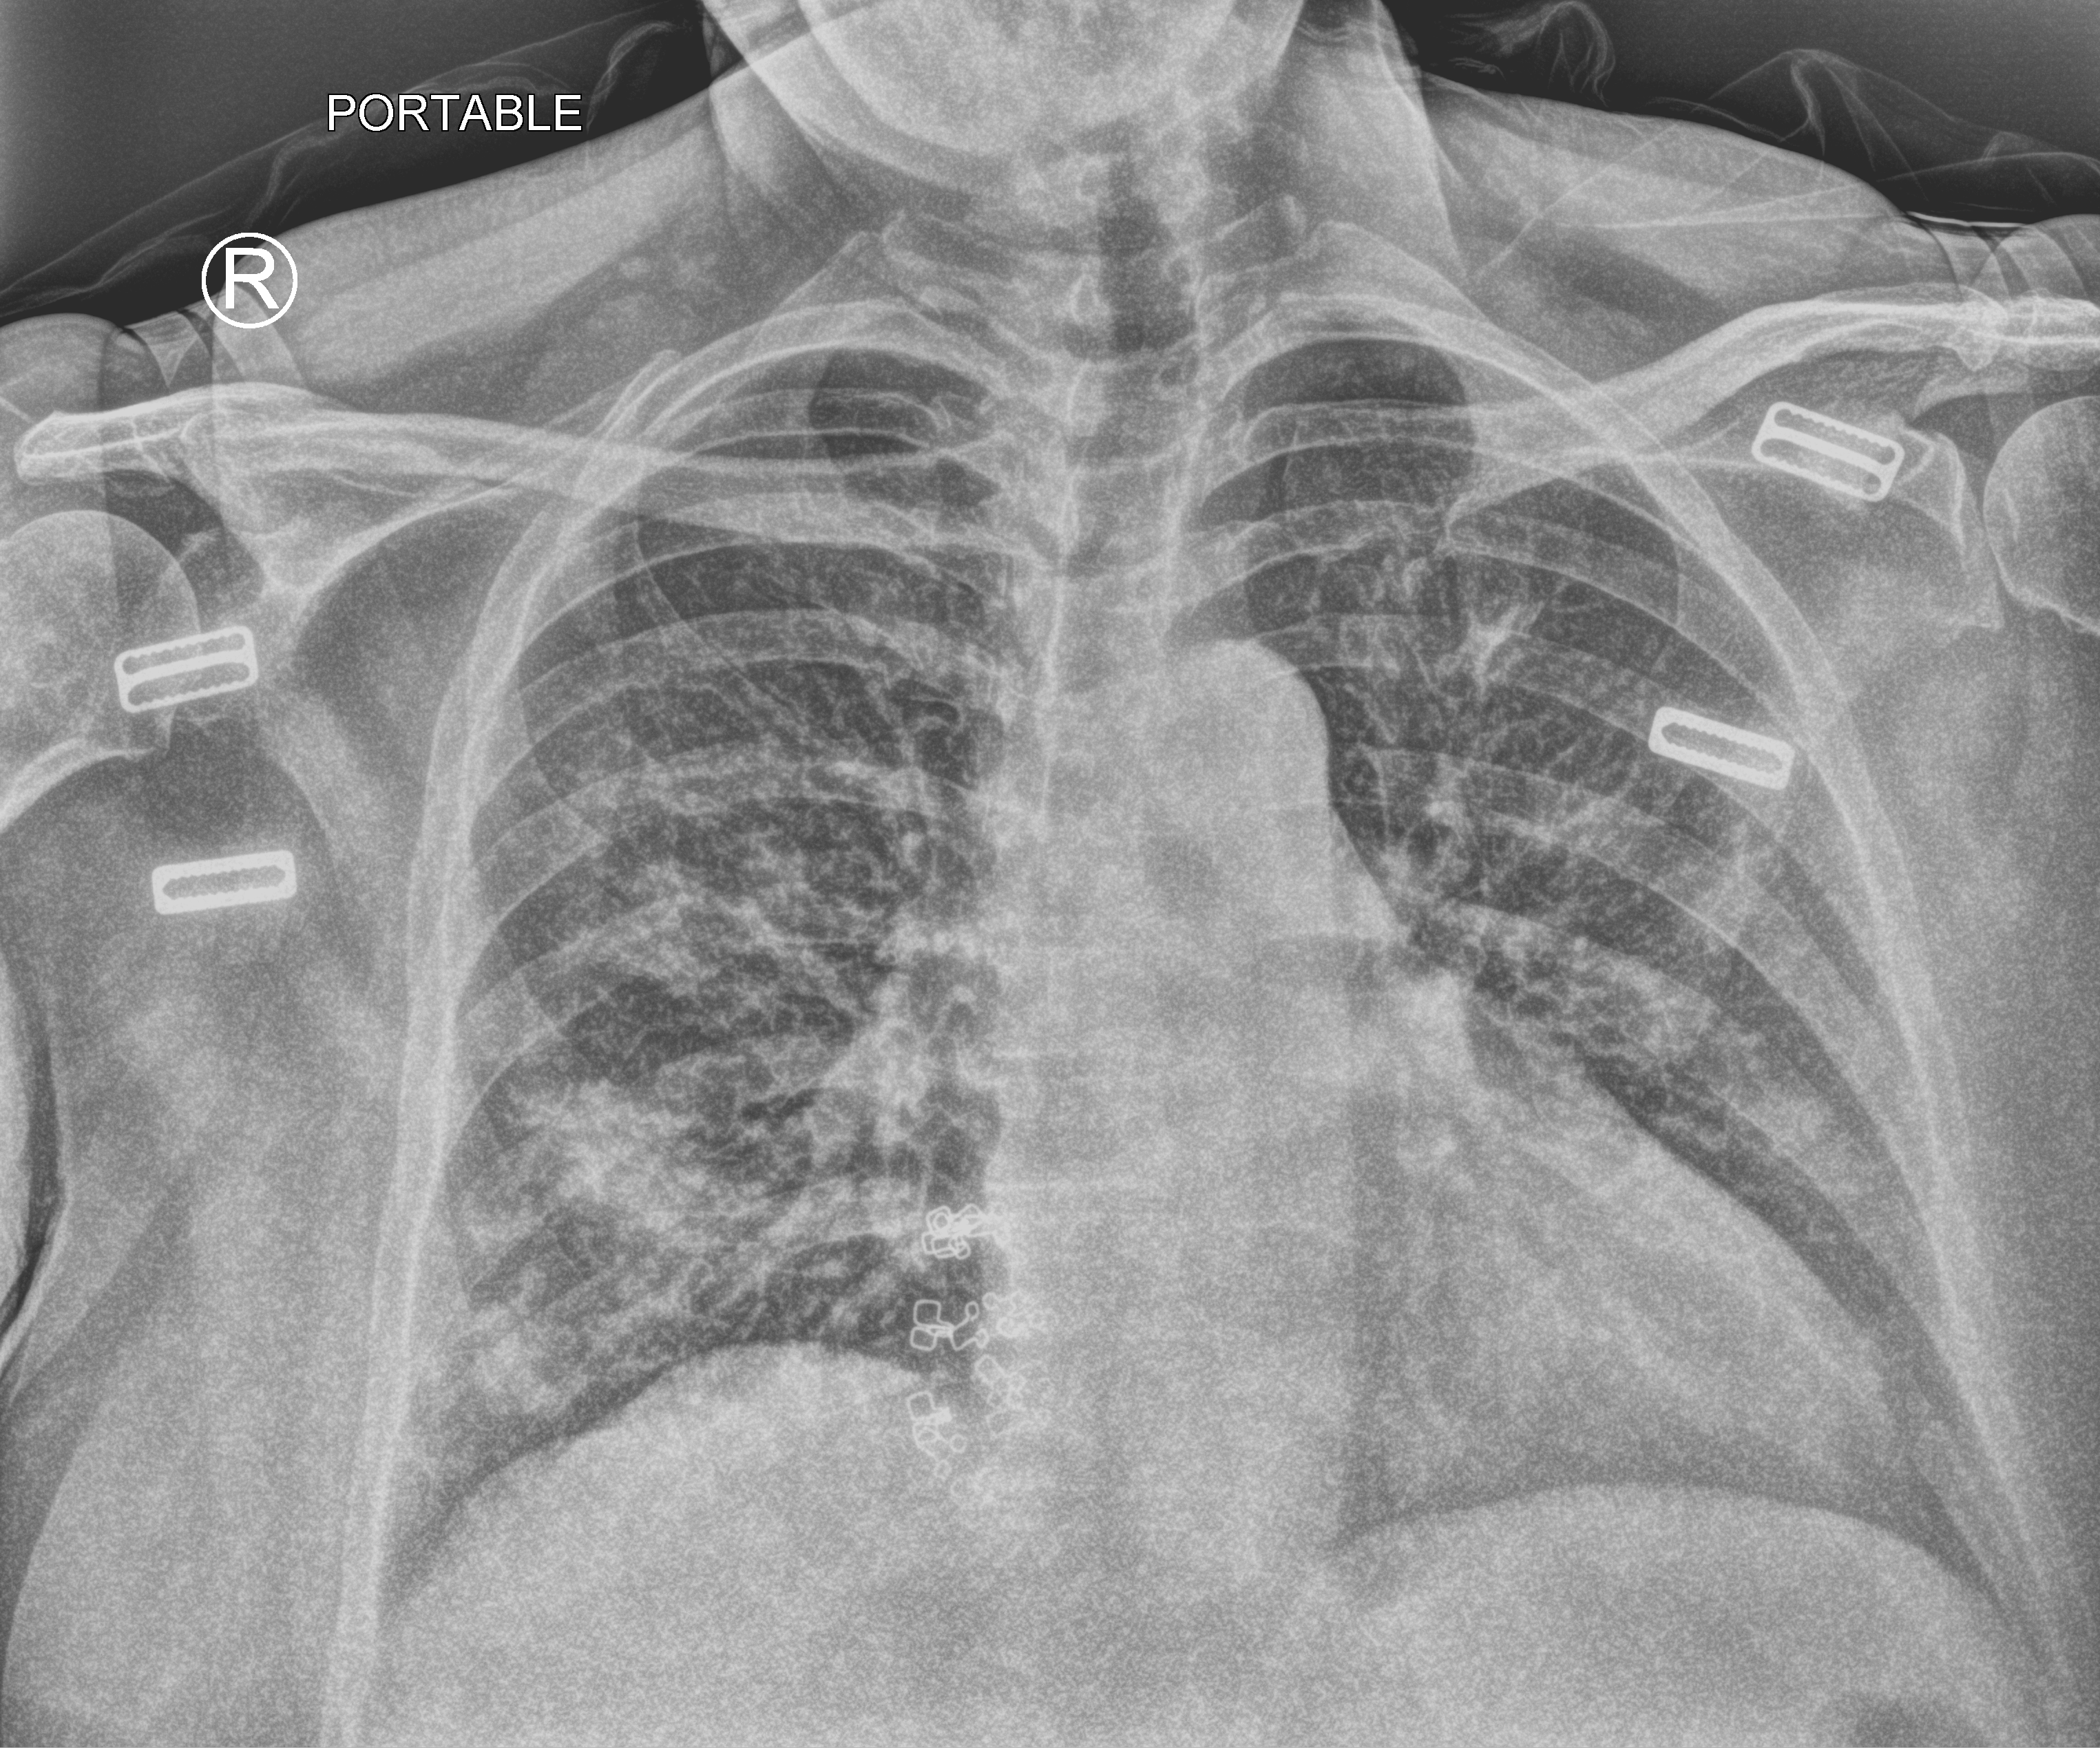
Bedside chest radiograph (computed radiography), anteroposterior (AP) projection. Female patient hospitalised with COVID-19, age 60–74 years.
Admission-level facts for this patient (not findings on this image; timing relative to this image not recorded): hypertension (admission record): yes.